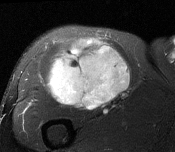
MRI of an extremity soft-tissue mass, one axial slice; slice 100 of 116 in the series (ordered by position); T2-weighted fat-saturated; MR volume resampled by the dataset authors to the PET/CT grid (not the native acquisition matrix); 3.27 mm slice thickness; 175 × 152 image matrix, field of view 171 × 148 mm. Male patient. From the clinical record (not read from this slice): histological type: pleiomorphic leiomyosarcoma; grade: intermediate; site of the primary tumour: right thigh.
Structures marked on this image (expert contour drawn on MRI and transferred to this co-registered scan by the dataset authors):
- gross tumour volume including surrounding oedema: bounding box <47,38,130,110> (left, top, right, bottom; pixels)
- gross tumour volume (mass): <49,40,130,110>